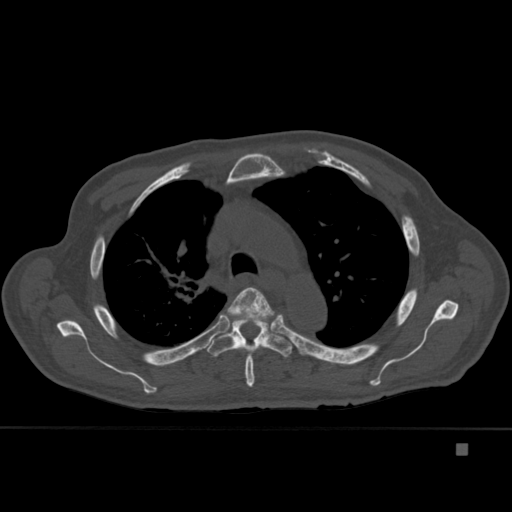
CT including the spine, one axial slice; slice 313 of 451 in the series (ordered by position); bone window (W 1800 / L 400 HU); 512 × 512 image matrix, field of view 378 × 378 mm. Male patient, age 75 years. Case-level facts recorded for this patient, not image findings: primary cancer: prostate.
Annotated regions visible in this slice (semi-automatic segmentation, software-assisted and operator-edited):
- T4 vertebra: bounding box <227,287,279,387> (left, top, right, bottom; pixels)
- T5 vertebra: <207,312,293,359>